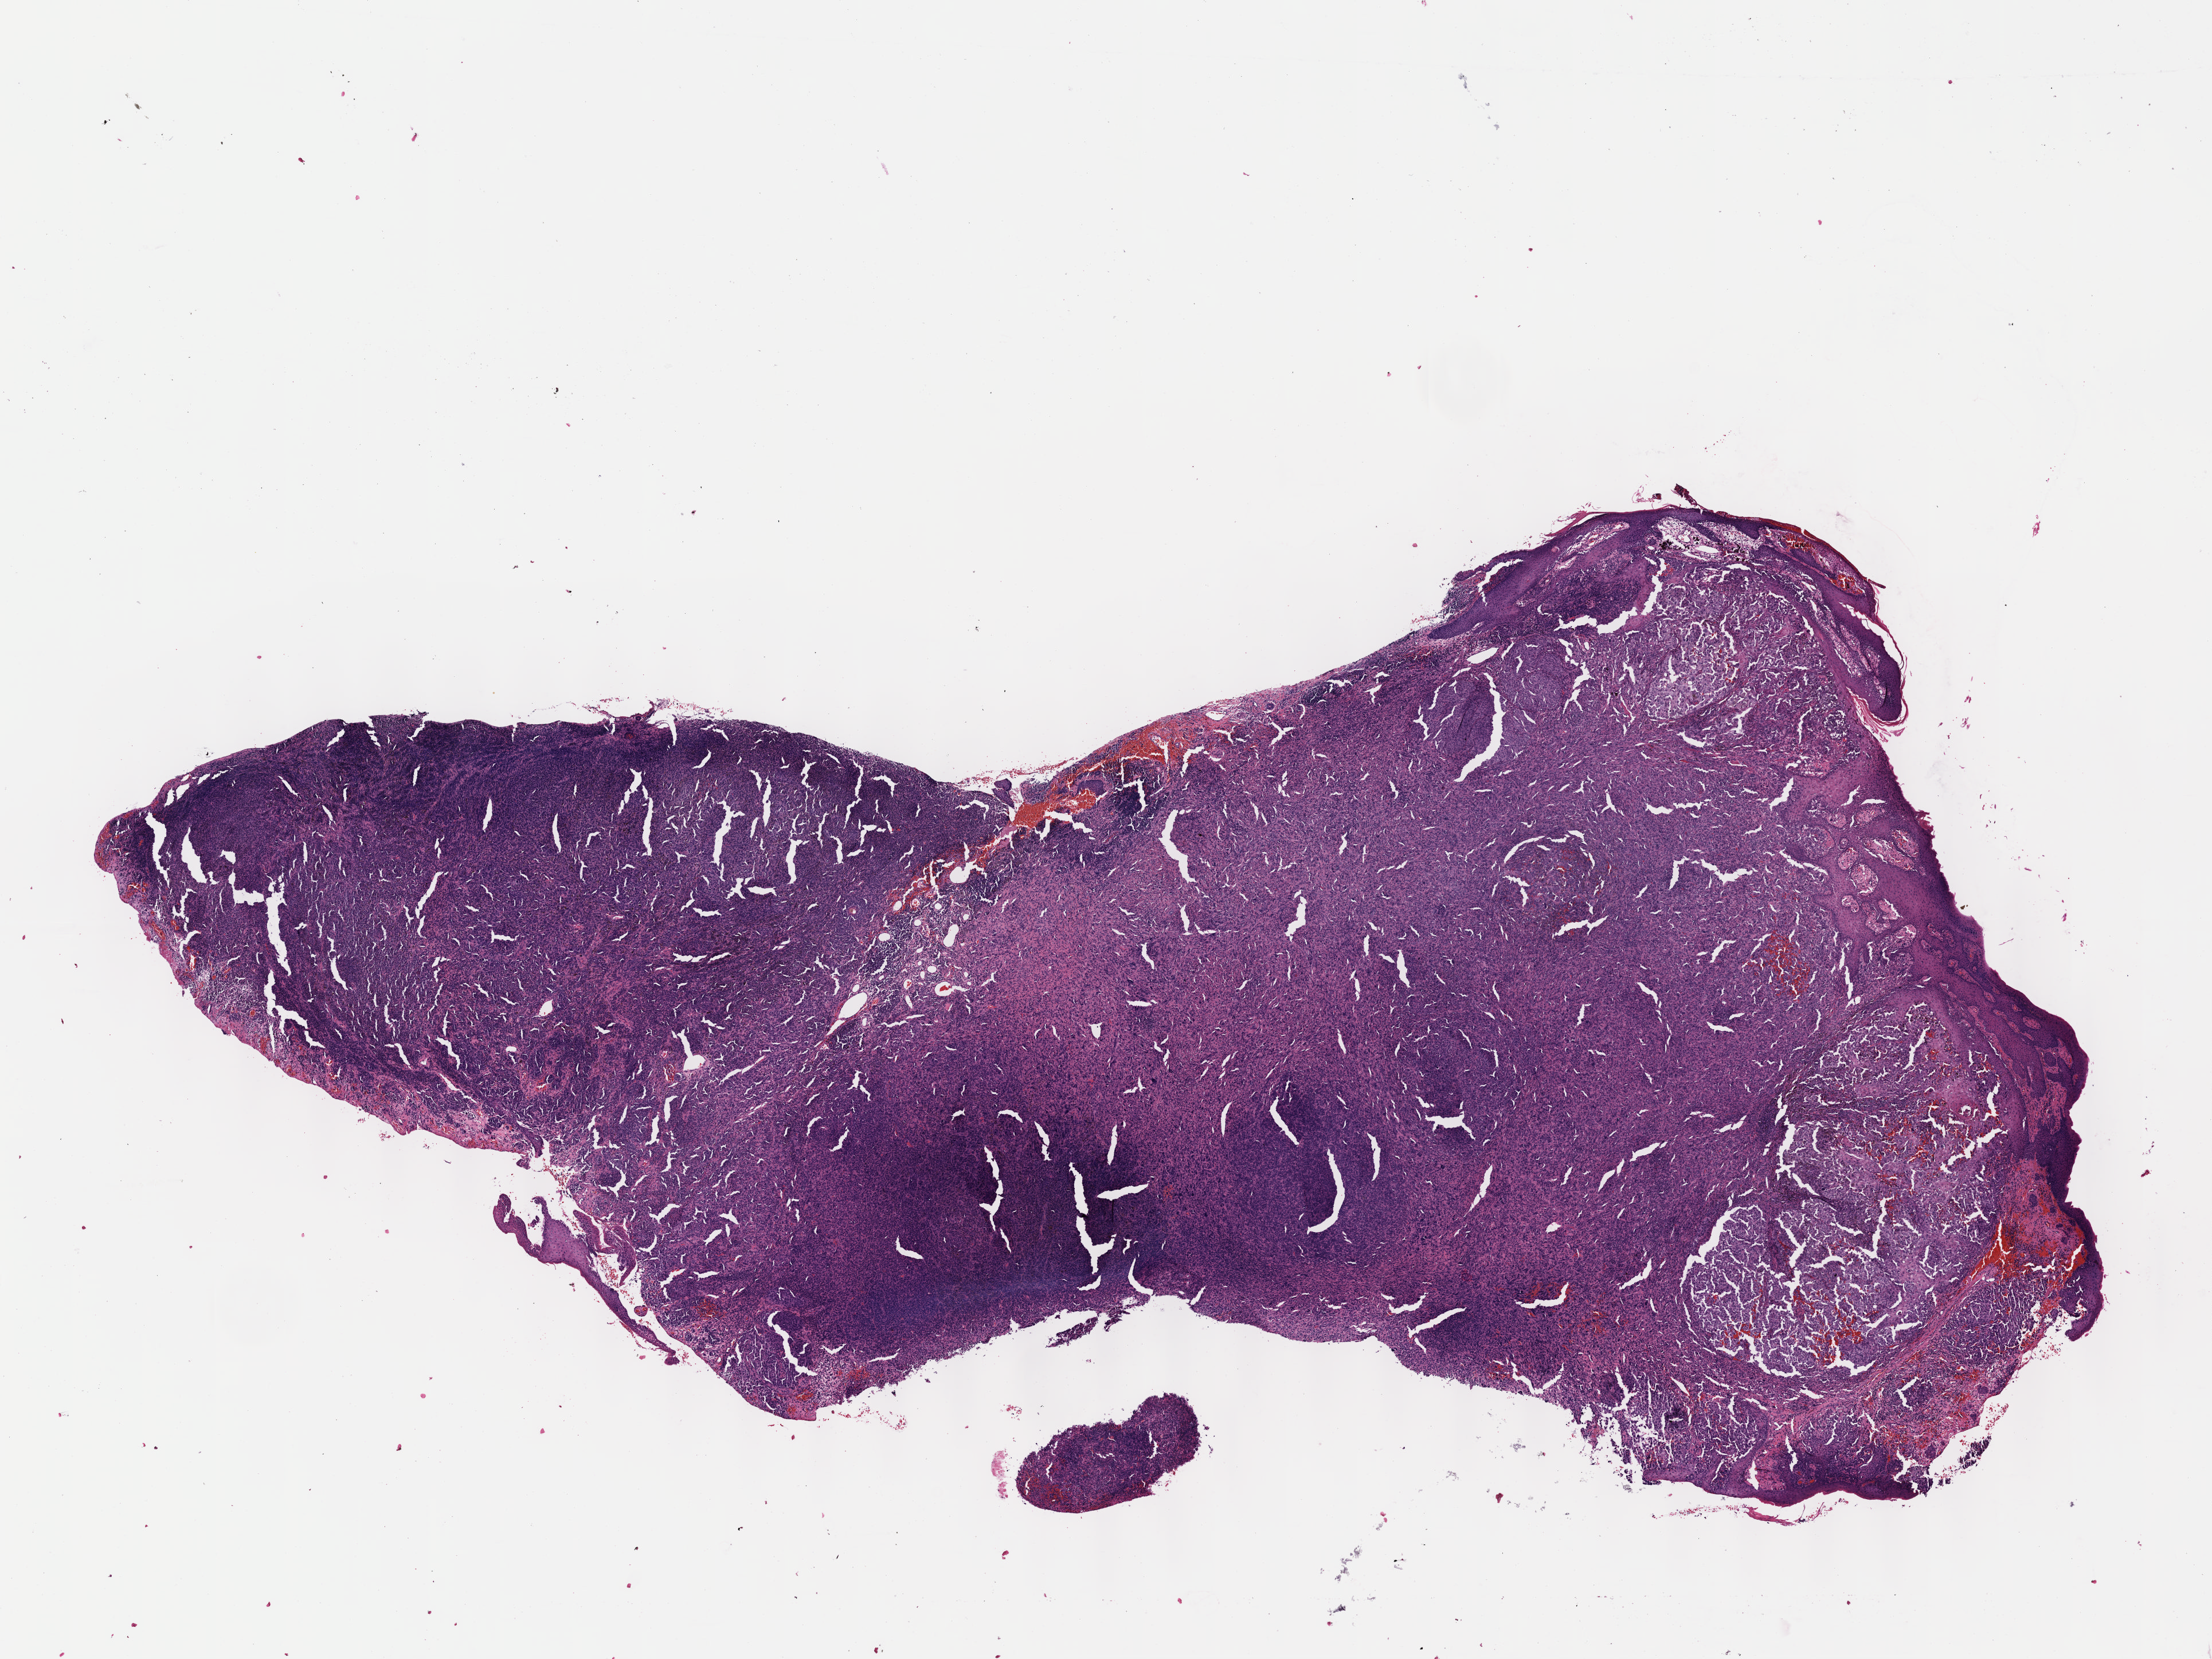
Digitized H&E-stained tissue section (whole slide) — low-resolution overview of the scanned area, about 15.6 x 11.7 mm (from a 40x scan), formalin-fixed paraffin-embedded (FFPE) diagnostic section, sample: primary tumour, skin. Male patient; age at initial diagnosis 65 years.
Histologic diagnosis: Malignant melanoma, NOS. AJCC pathologic stage: IIC. TNM: T4b N0 M0.